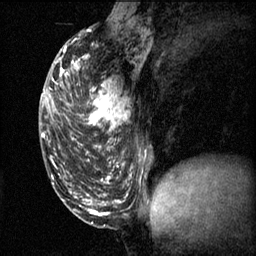
Breast MRI (dynamic contrast-enhanced), one sagittal slice; position 26 of 60 along the scan axis; 3 images stored at this slice position (order not interpretable as contrast timing); 1.5 T; TE 4.2 ms, TR 11.1 ms; 2 mm slice thickness; 256 × 256 image matrix, field of view 180 × 180 mm. Female patient, age 50 years.
Annotated regions visible in this slice (semi-automatic segmentation, software-assisted and operator-edited):
- analysis volume of interest (the breast-tissue region the enhancement analysis was run in; not a lesion): bounding box [x1, y1, x2, y2] px = [68, 68, 138, 141]
- tumour enhancement mask (voxels above the 70 % enhancement threshold inside the analysis volume of interest): [68, 68, 130, 141]